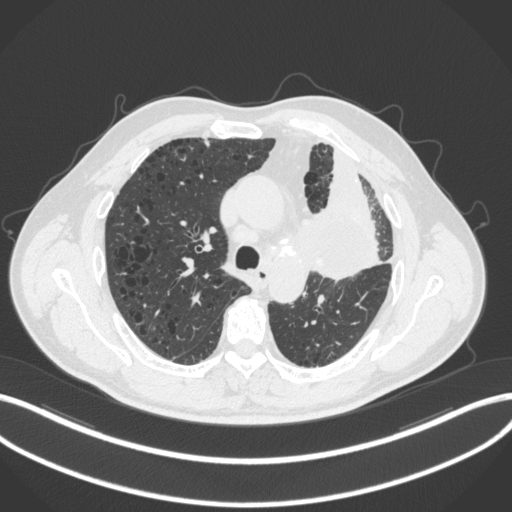
Chest CT, one axial slice; position 200 of 286 along the scan axis; reconstruction kernel B31f; 120 kVp; lung window (W 1500 / L -600 HU); 1 mm slice thickness; 512 × 512 image matrix, field of view 400 × 400 mm. Patient: male, 68 years. Case-level facts recorded for this patient, not image findings: clinical TNM (as recorded): T3 N3 M1.
Annotated regions visible in this slice (rectangle marked by the reading radiologist):
- lung tumour (recorded histology: adenocarcinoma): bounding box (x1, y1, x2, y2) in pixels: (297, 187, 383, 283)